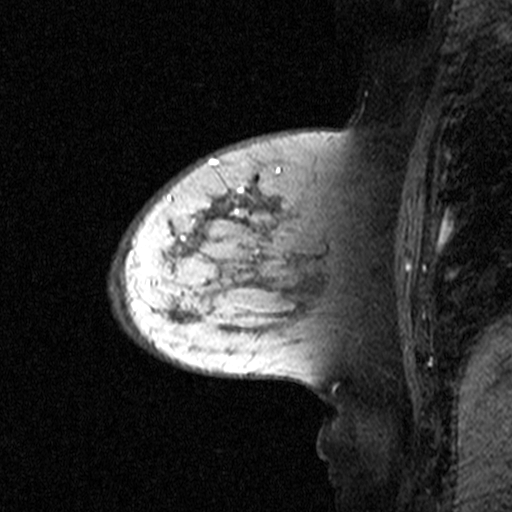
Breast MRI (dynamic contrast-enhanced), one sagittal slice. Position 16 of 44 along the scan axis. Dynamic contrast-enhanced study with each time point stored as its own series, time point 2 of 3 at this slice position (early post-contrast, ordered by acquisition time). 1.5 T. TE 4.5 ms, TR 11 ms. 3 mm slice thickness. 512 × 512 image matrix, field of view 200 × 200 mm. Female patient, age 65 years. From the clinical record (not read from this slice): setting: breast cancer imaged before/during neoadjuvant chemotherapy; receptor status: HER2-positive.
Outlined on this slice (semi-automatically segmented with operator editing):
- analysis volume of interest (the breast-tissue region the enhancement analysis was run in; not a lesion): bounding box [x1, y1, x2, y2] px = [160, 172, 329, 345]
- tumour enhancement mask (voxels above the 90 % enhancement threshold inside the analysis volume of interest): [198, 186, 263, 252]